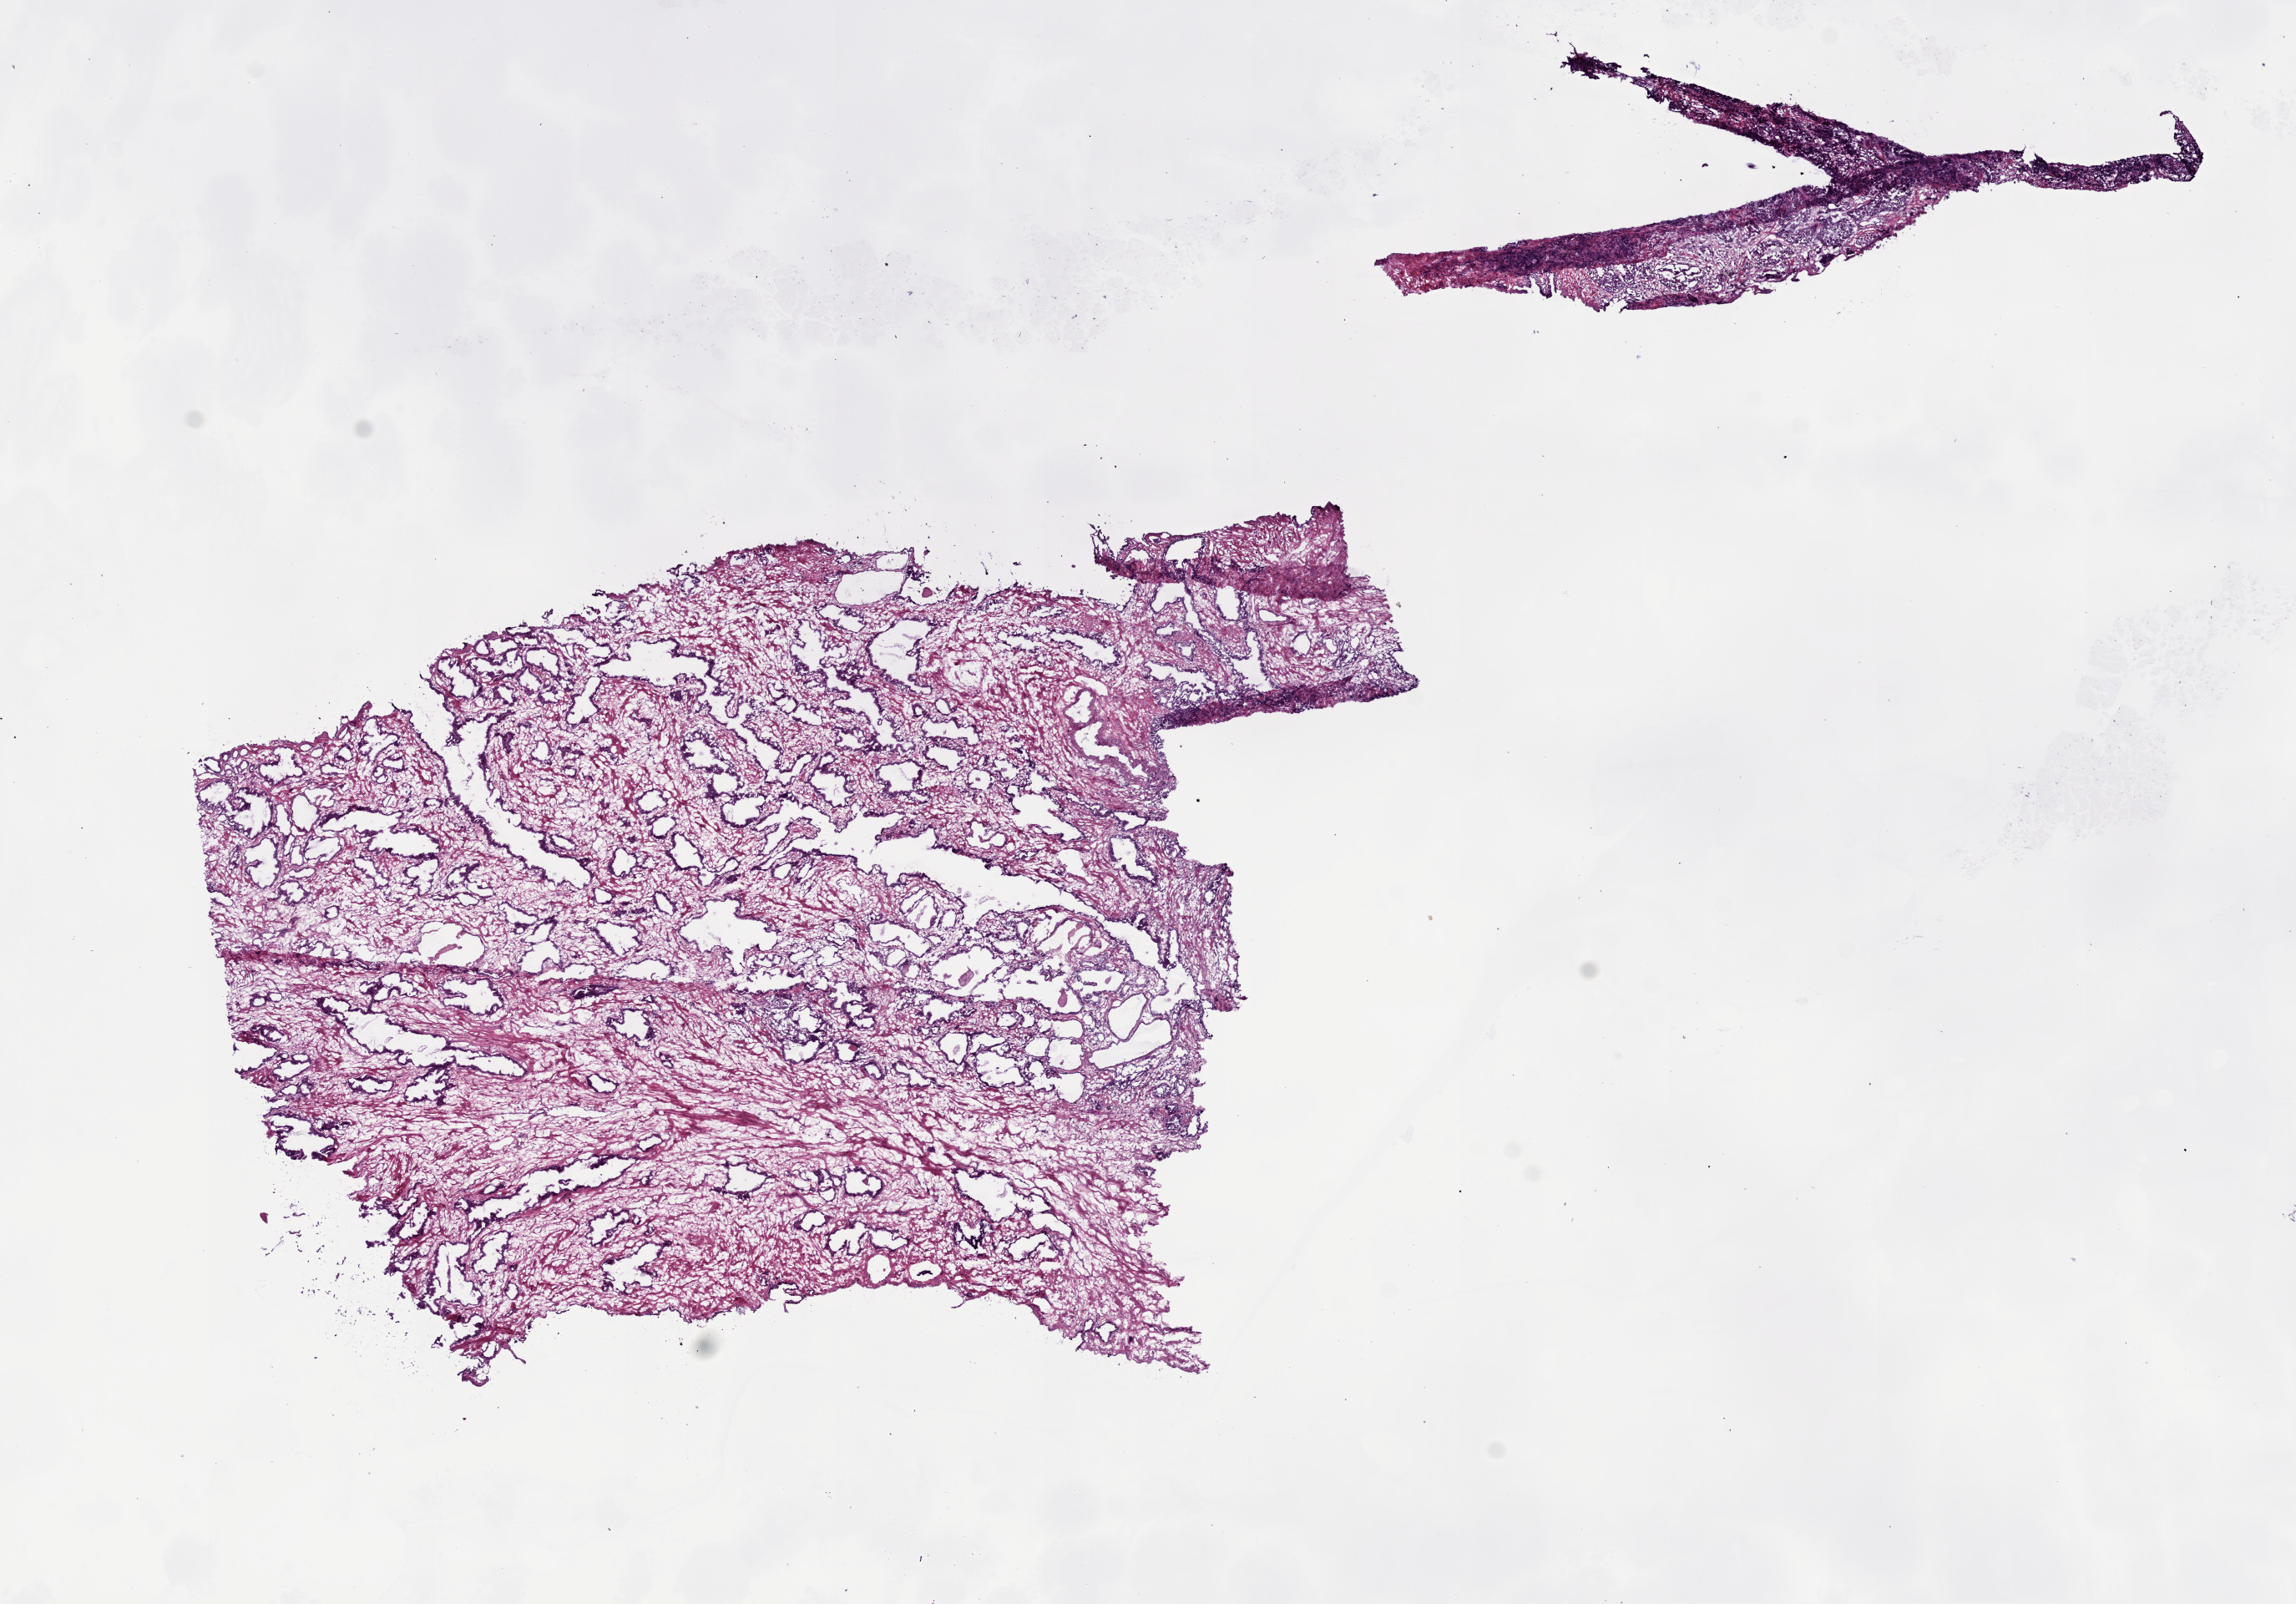
Digitized H&E tissue section (whole slide), a low-resolution overview of the entire scanned area, about 11.0 x 7.7 mm (acquisition: 20x scan). Frozen section. Prostate, primary tumour sample. Patient: male, age at initial diagnosis 61 years. Gleason score: 7 (4+3). Composition of this section per pathologist review: tumour cells 1%, tumour nuclei 2%, normal cells 40%, stromal cells 49%, necrosis 0%. Infiltration values recorded for this section: lymphocyte infiltration 1%, monocyte infiltration 0%, neutrophil infiltration 0%.
Diagnosis: Acinar cell carcinoma (prostate gland). Laterality: bilateral.